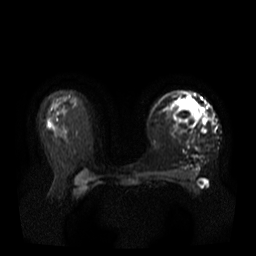
Breast MRI, one axial slice; position 24 of 37 along the scan axis; diffusion-weighted series; image 2 of 4 stored at this slice position (different b-values; order by instance number); 3 T; 5 mm slice thickness; 256 × 256 image matrix, field of view 380 × 380 mm. Female patient.
Structures marked on this image (outlined manually by an expert reader):
- tumour on diffusion-weighted imaging: bounding box <201,117,207,133> (left, top, right, bottom; pixels)